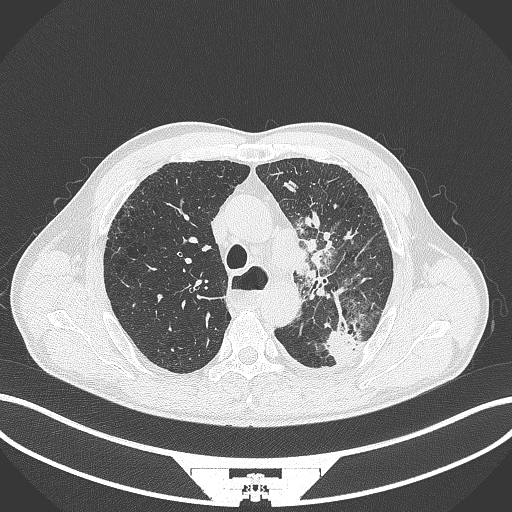
Chest CT, one axial slice; slice 283 of 411 in the series (ordered by position); reconstruction kernel B70f; 120 kVp; lung window (W 1500 / L -600 HU); 1 mm slice thickness; 512 × 512 image matrix, field of view 400 × 400 mm. Male patient, age 57 years. Case-level facts recorded for this patient, not image findings: clinical TNM (as recorded): T2a N1 M0.
Annotated regions visible in this slice (bounding box drawn by a radiologist):
- lung tumour (recorded histology: squamous cell carcinoma): bounding box (x1, y1, x2, y2) in pixels: (295, 239, 331, 282)